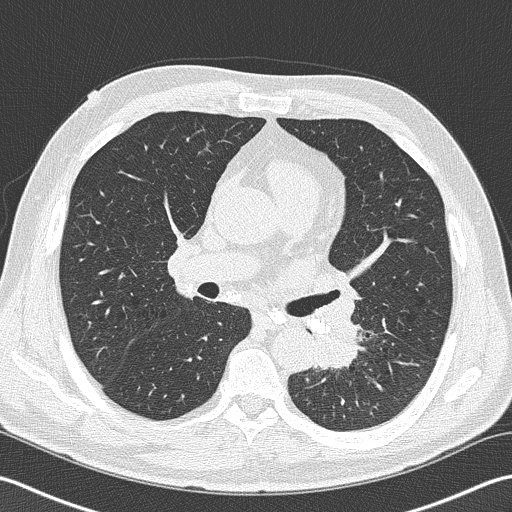
Low-dose screening chest CT, axial slice, second annual screen, lung window (W 1500 / L -600 HU), 2 mm slice thickness, 120 kVp, 512 × 512 image matrix. Male, age 57 years at enrolment. Former smoker at enrolment.
Lesion marked by an expert reader, box from (x=293, y=304) to (x=373, y=383) px. Reader record for this screening exam (exam-level; its link to the box is not recorded): non-calcified nodule or mass ≥4 mm, left lower lobe, 40 × 30 mm, spiculated (stellate) margins, soft tissue attenuation, pre-existing on the prior screen: no. Later outcome: lung cancer diagnosed 9 days after this screen — squamous cell carcinoma, NOS, left lower lobe, moderately differentiated (G2), stage IIIB (AJCC 6th edition), 38 mm at pathology.